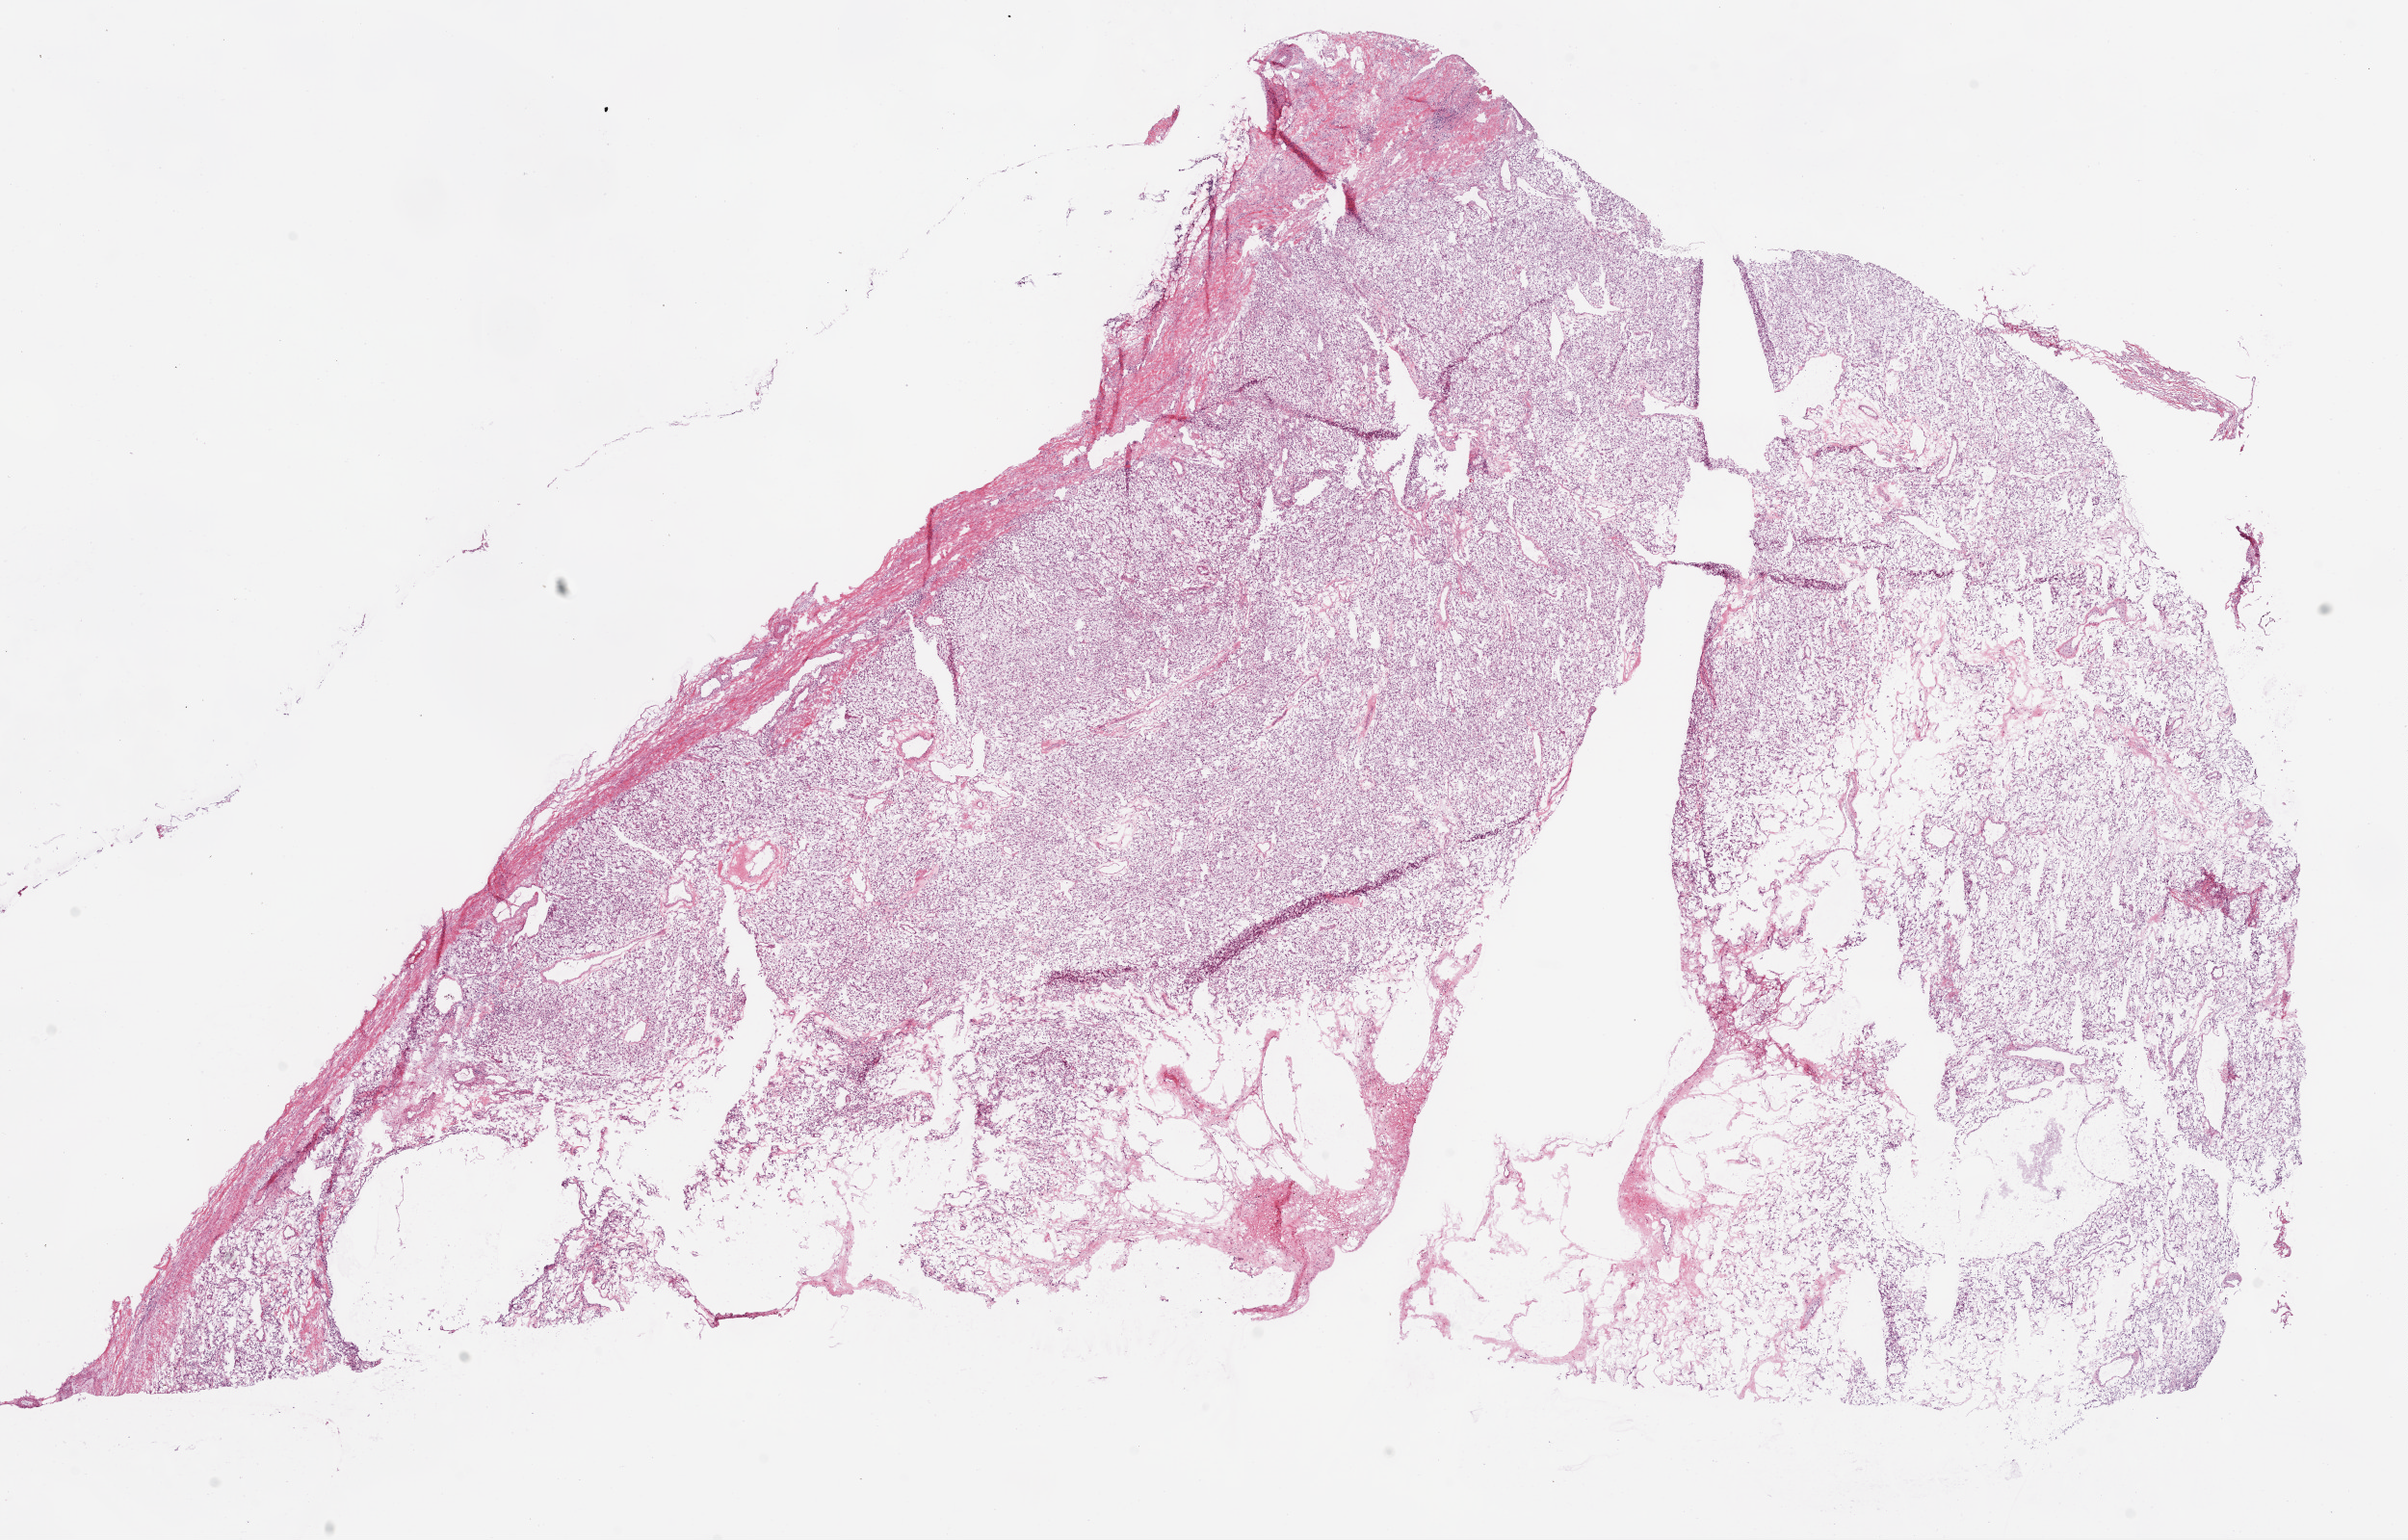
Whole-slide histology image, H&E-stained, shown as a low-resolution overview of the whole scanned area (about 20.1 x 12.8 mm, slide scanned at 20x); frozen section from the bottom of the tissue portion; sample: primary tumour, kidney. Male patient; age at initial diagnosis 58 years.
Histologic diagnosis: Clear cell adenocarcinoma, NOS.